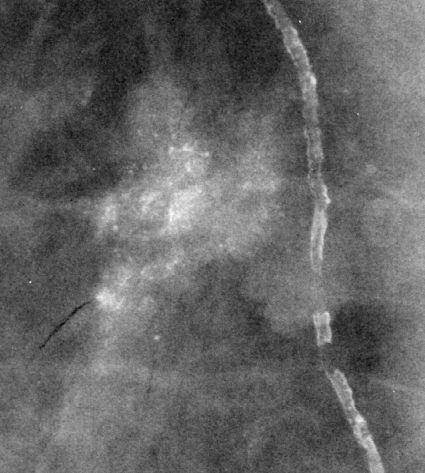
Cropped region of a digitized screen-film mammogram centred on a radiologist-marked abnormality, right breast, MLO view, BI-RADS breast density category 3 (scale 1–4).
- Finding: calcifications, morphology punctate / pleomorphic, distribution clustered; BI-RADS assessment category 4; subtlety rating 3 on a 1 (subtle) to 5 (obvious) scale; pathology (as recorded): malignant.